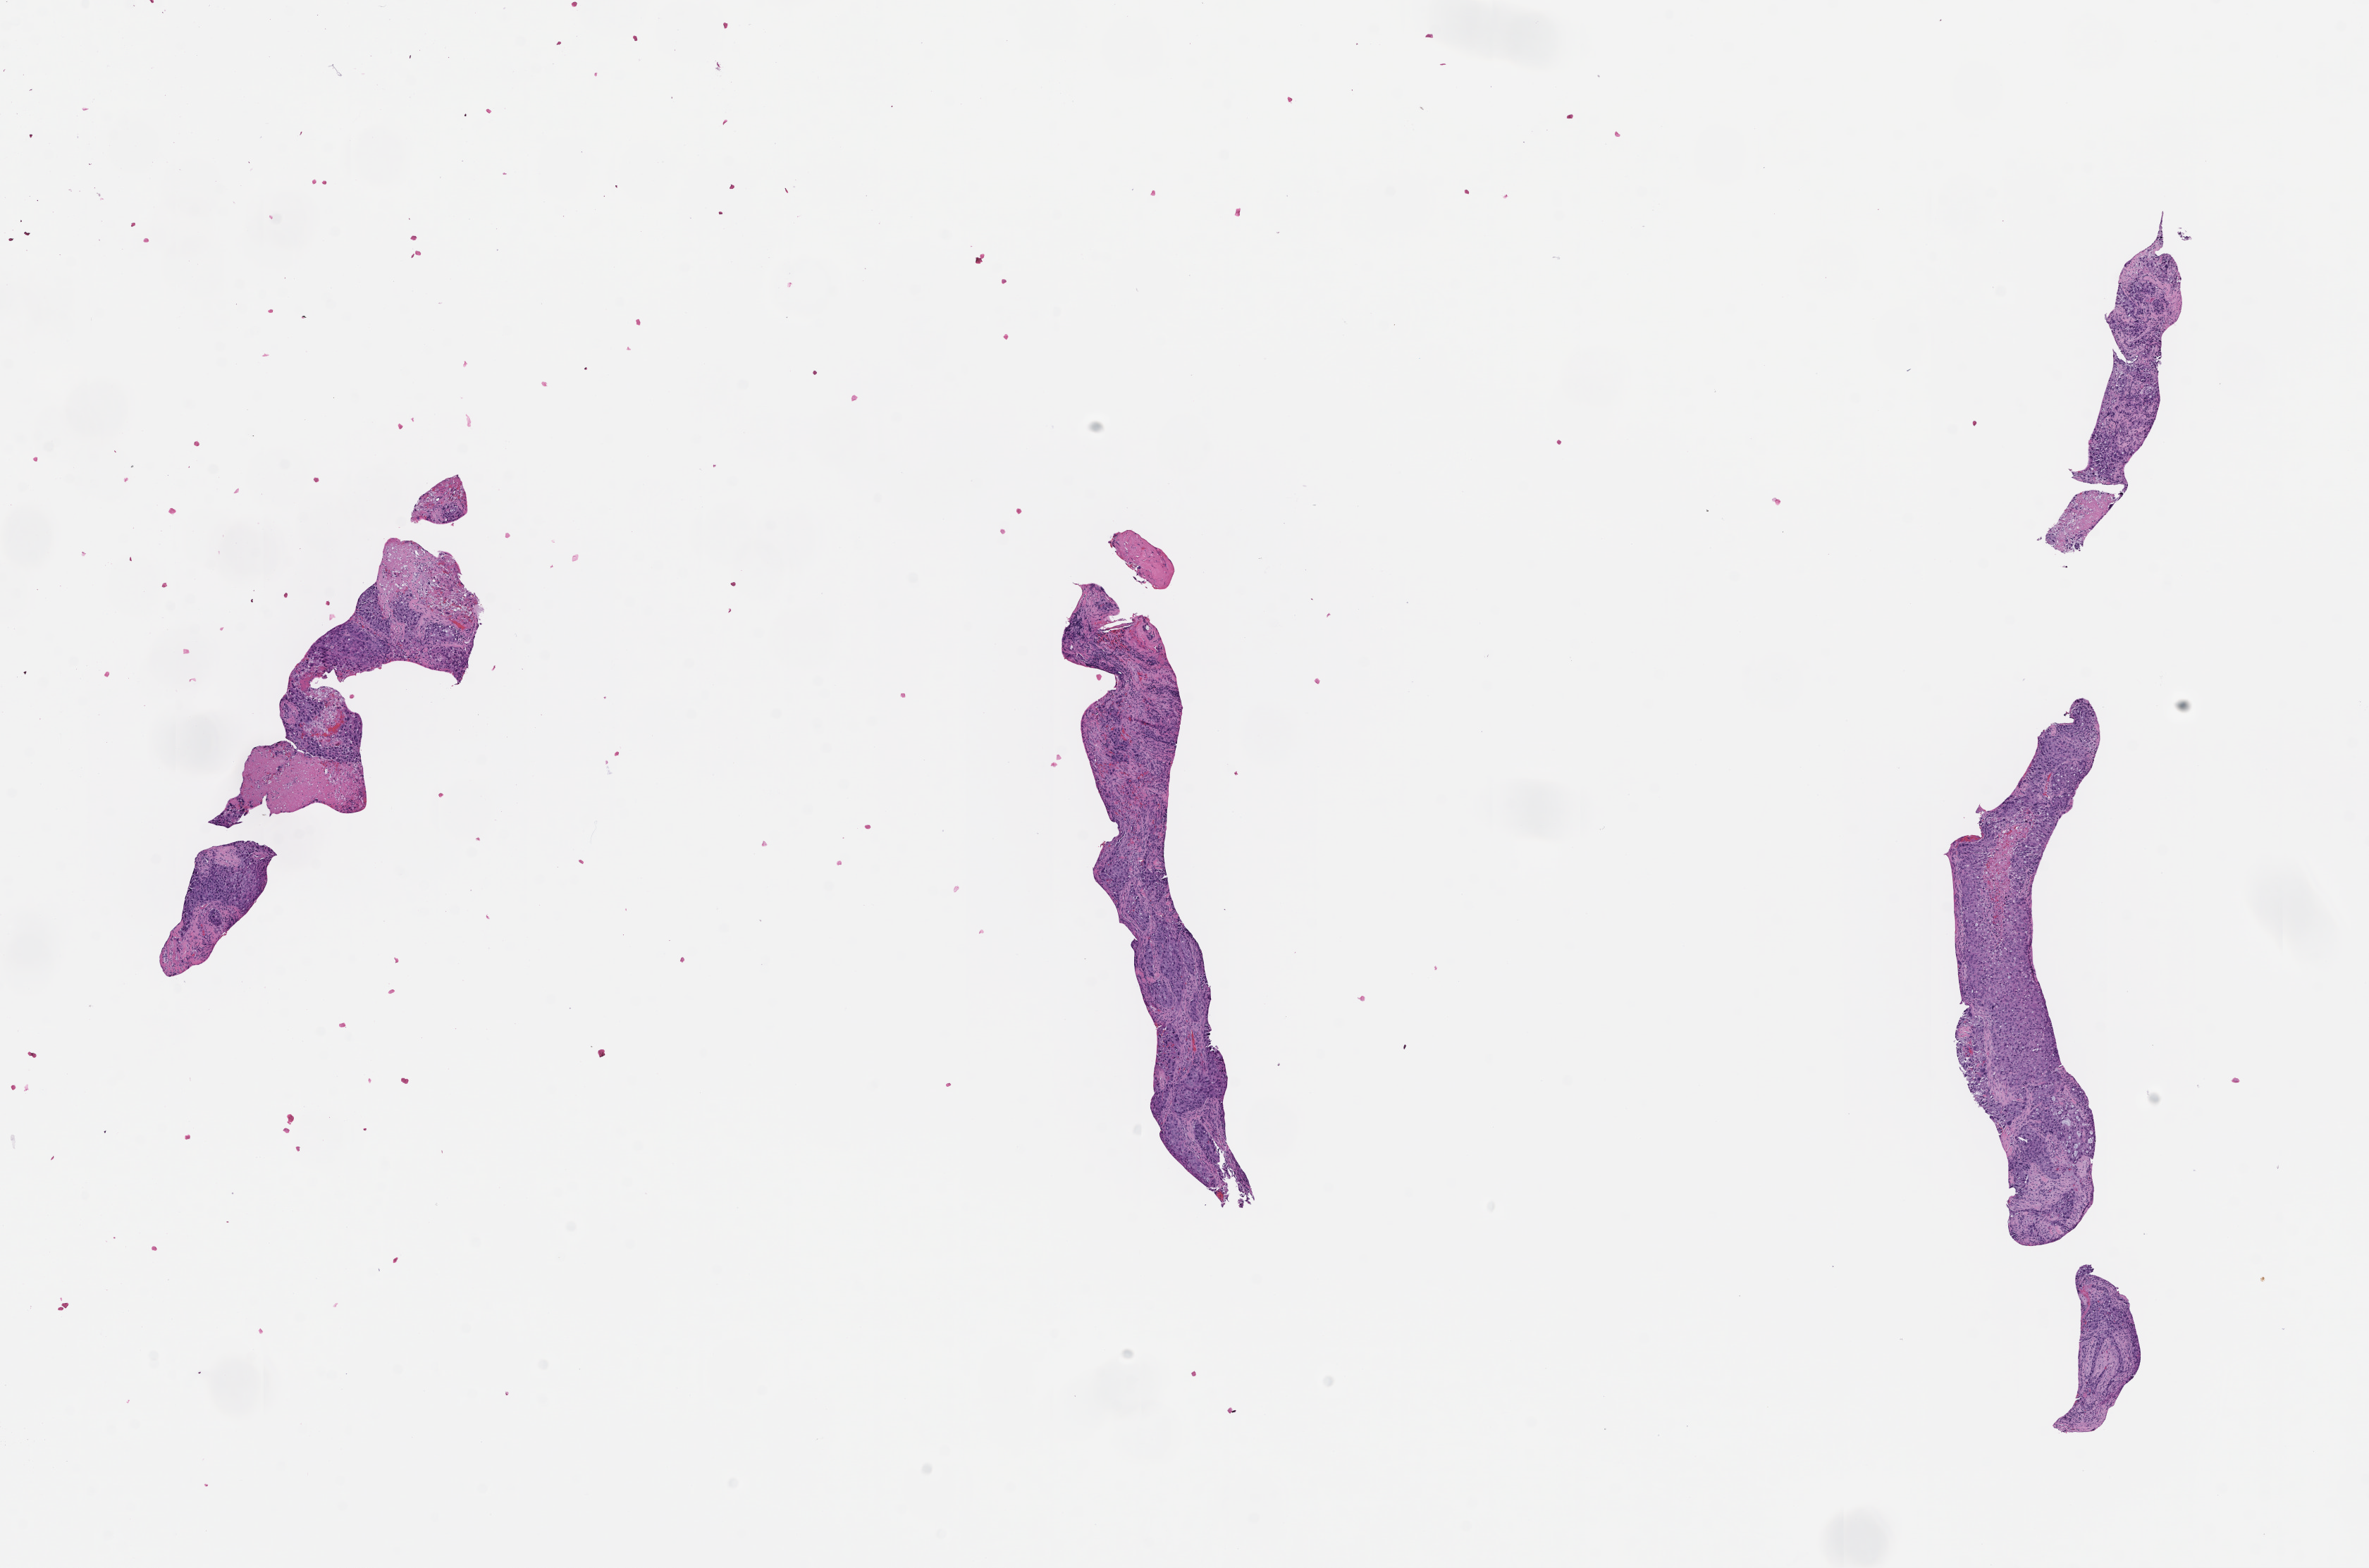
Whole-slide image, H&E stain — a low-resolution overview of the entire scanned area, about 13.6 x 9.0 mm. Formalin-fixed, paraffin-embedded (FFPE) tissue. Site: lung. Collected at baseline (before treatment). Male patient.
This section: primary tumour tissue. Diagnosis: Non-Small Cell Lung Carcinoma.